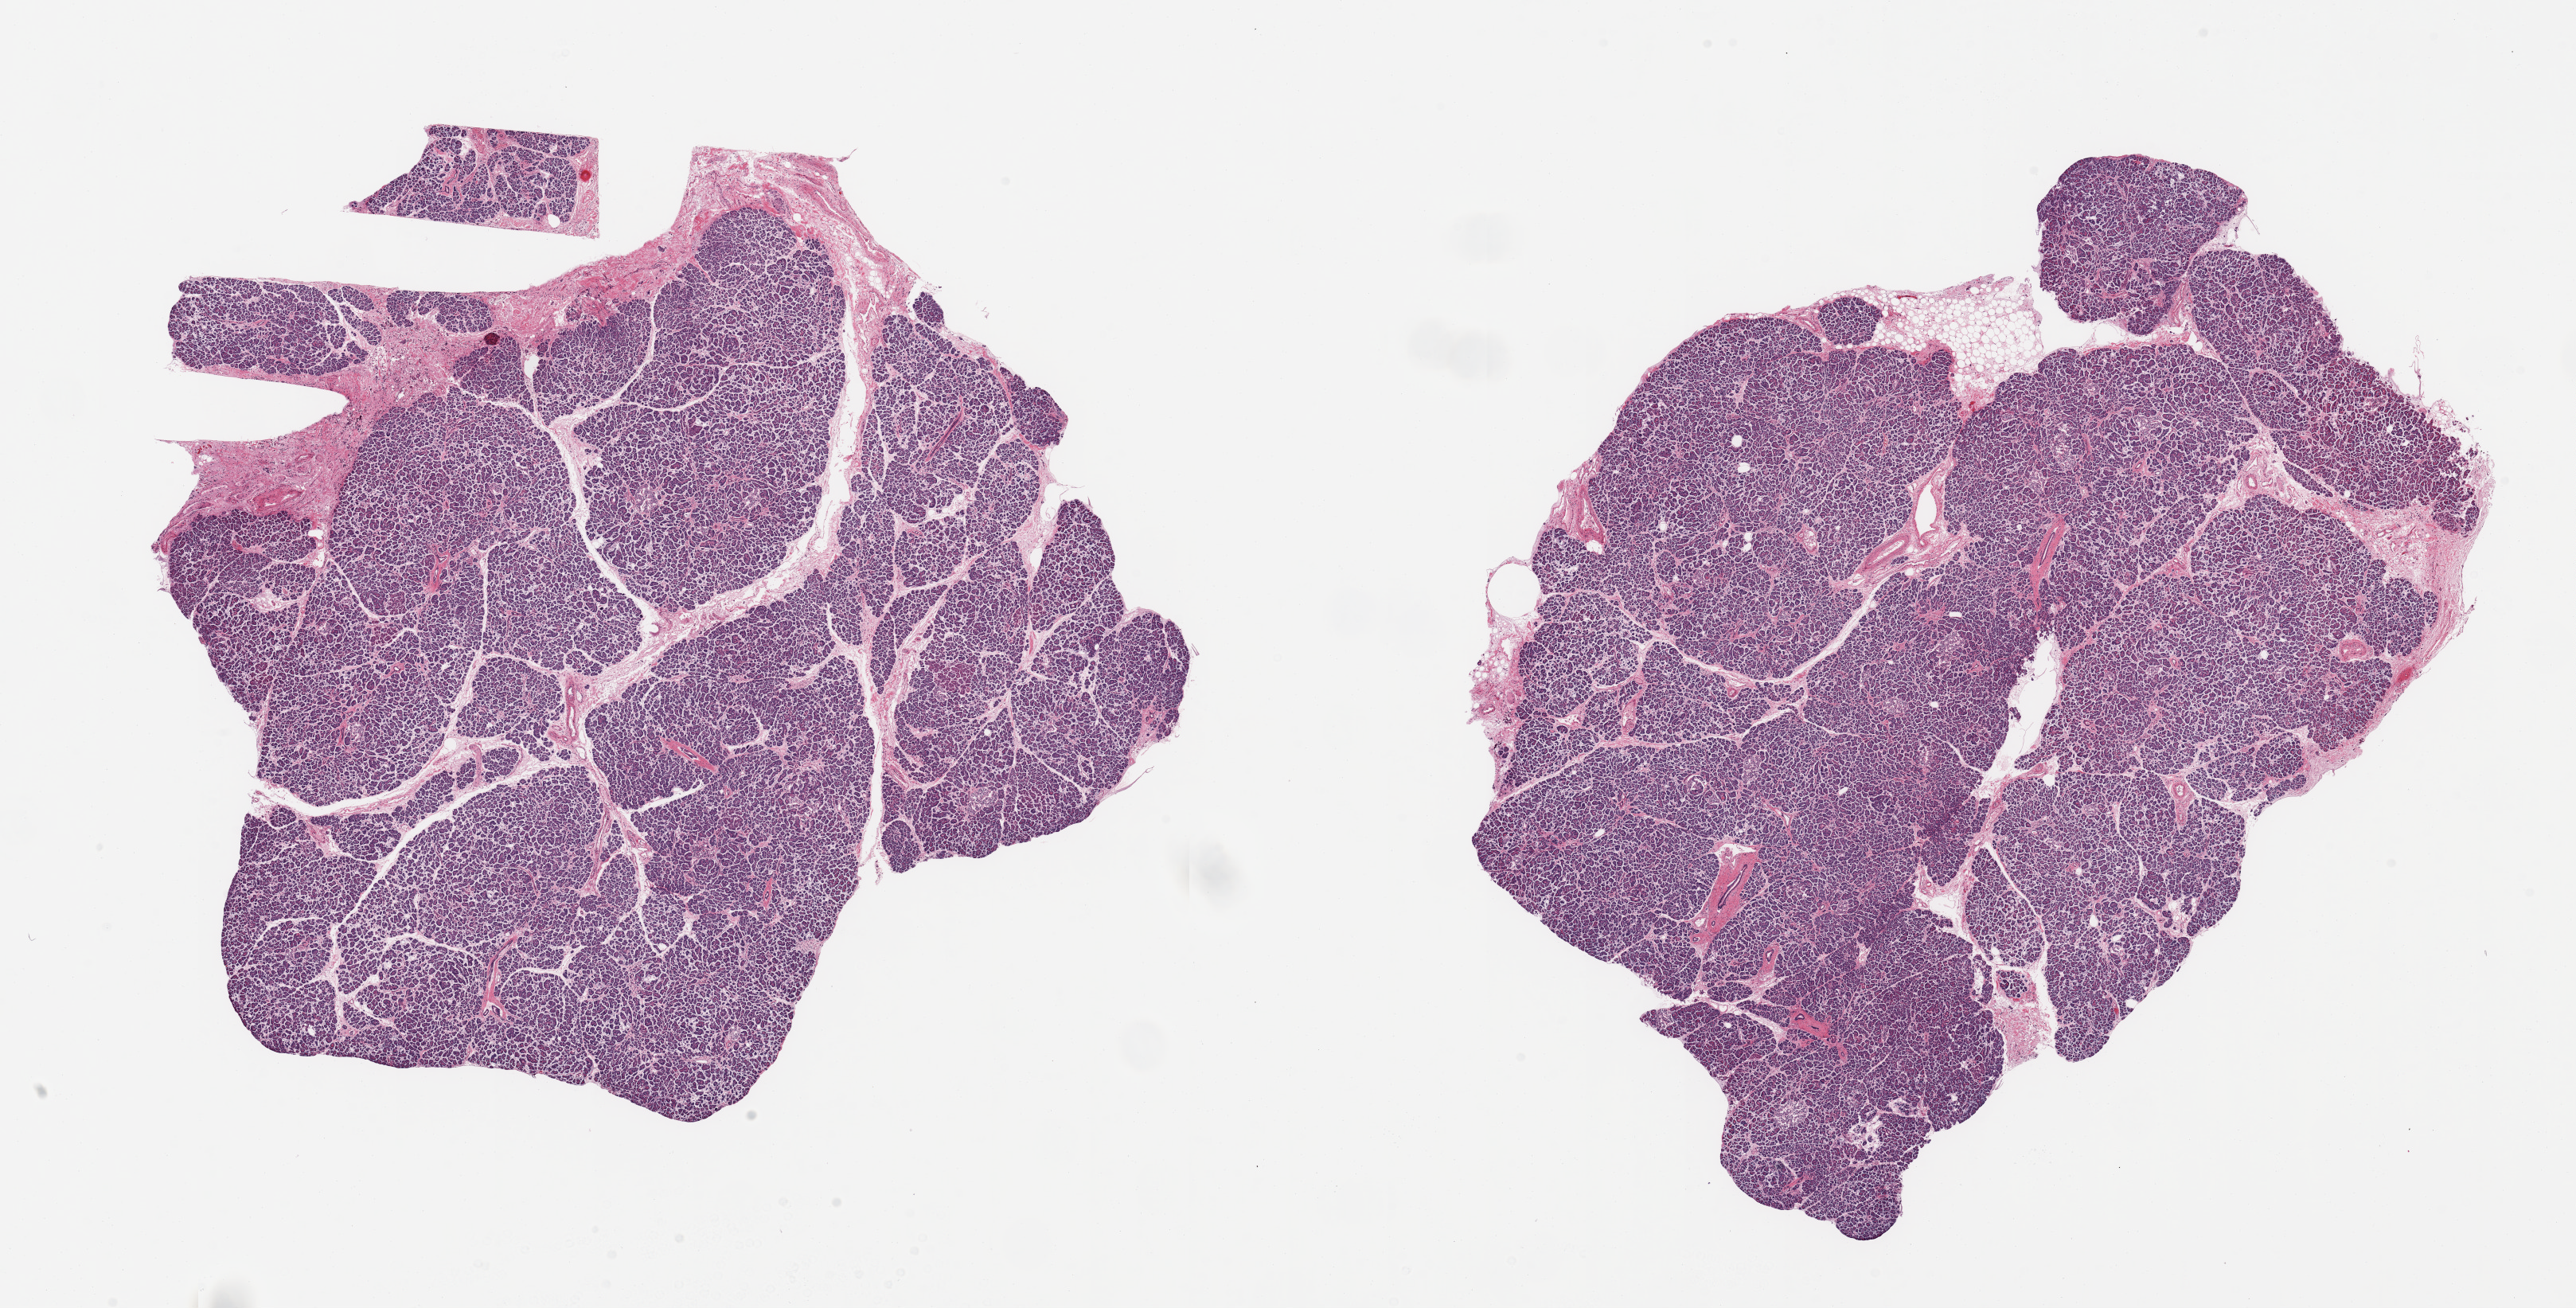
Hematoxylin and eosin (H&E) whole-slide image — shown as a low-resolution overview of the whole scanned area (about 25.6 x 13.0 mm). PAXgene-fixed, paraffin-embedded tissue. Section of pancreas (target tissue). Donor tissue sample.
Review note (as recorded): 2 pieces, moderately advanced saponification; islets still dimly visible, advanced degeneration.